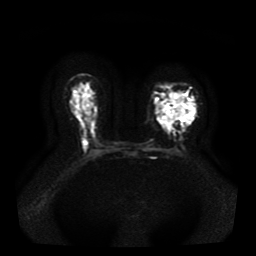
Breast MRI, one axial slice. Position 24 of 41 along the scan axis. Diffusion-weighted series; image 2 of 4 stored at this slice position (different b-values; order by instance number). 1.5 T. 5 mm slice thickness. 256 × 256 image matrix, field of view 330 × 330 mm. Female patient.
Outlined on this slice (outlined manually by an expert reader):
- tumour on diffusion-weighted imaging: box from (x=155, y=93) to (x=191, y=129) px